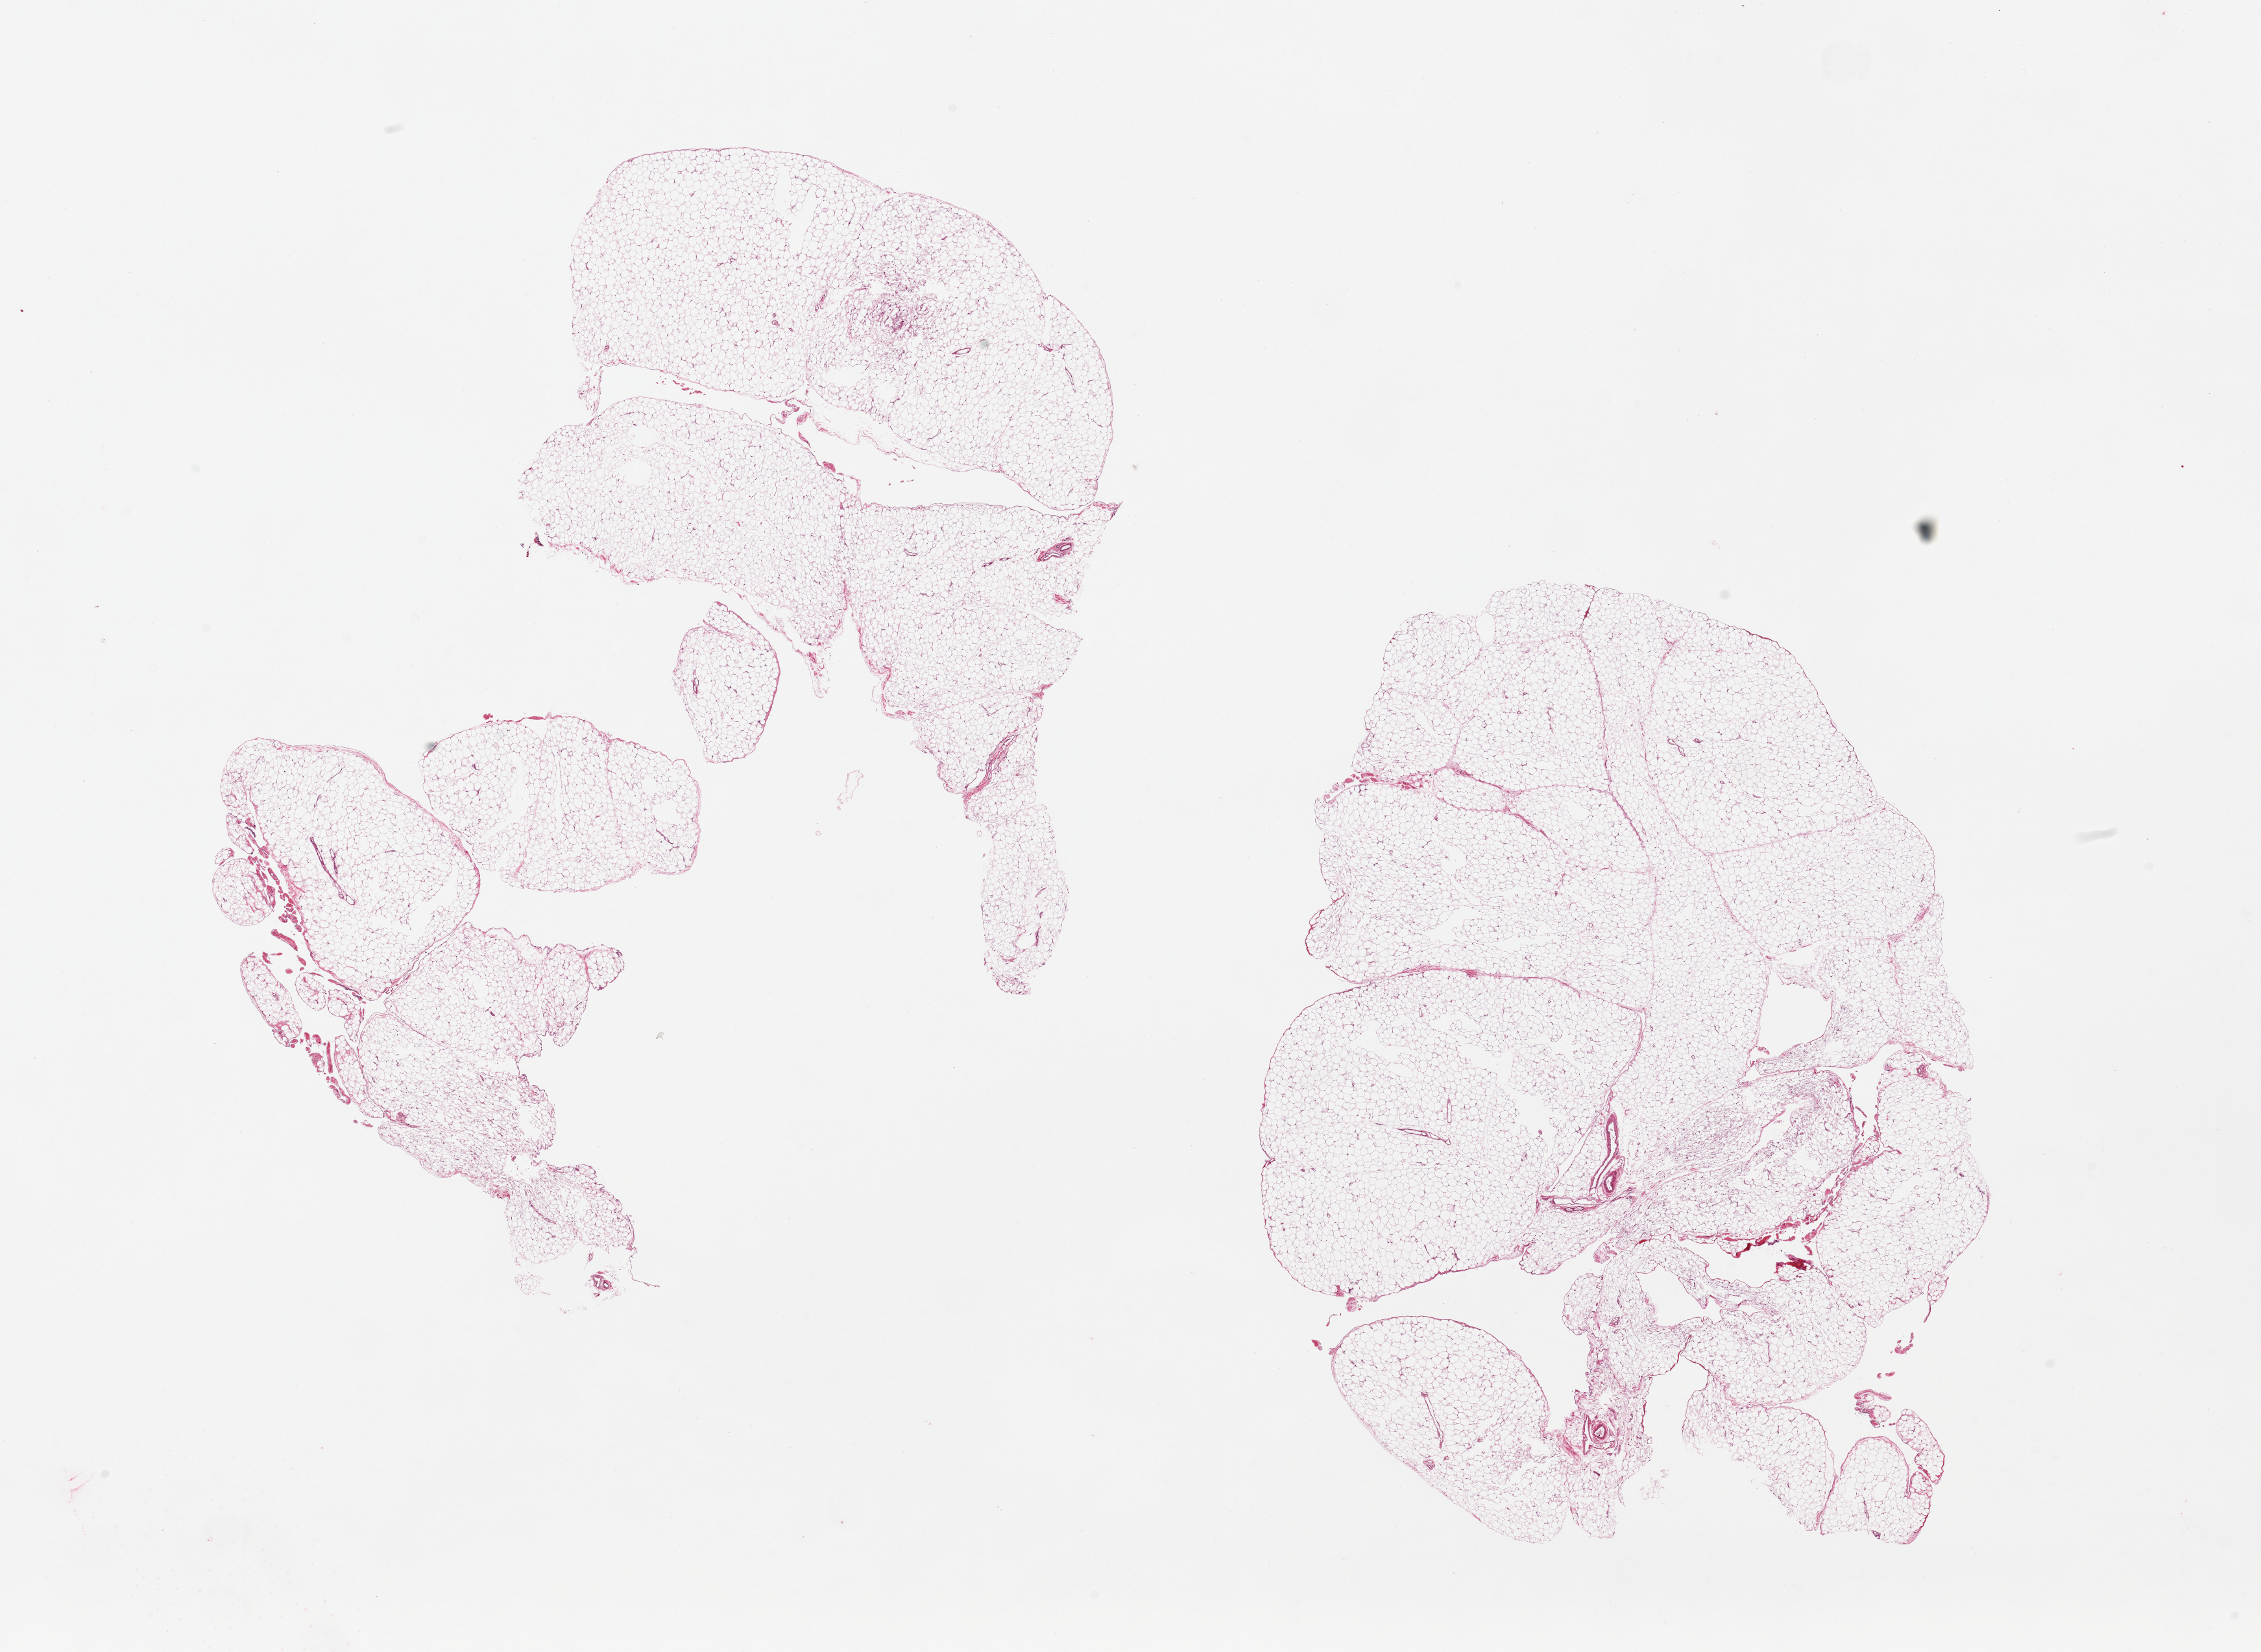
Whole-slide image, haematoxylin and eosin stain, brightfield, shown as a low-resolution overview of the whole scanned area (about 27.6 x 20.1 mm, slide scanned at 20x), PAXgene-fixed, paraffin-embedded tissue, sampled site (target tissue): omentum, donor tissue sample. Donor: male.
• pathologist's review note for this sample: 2 pieces, essentially all fat, limited fibrous tissue/small vessels